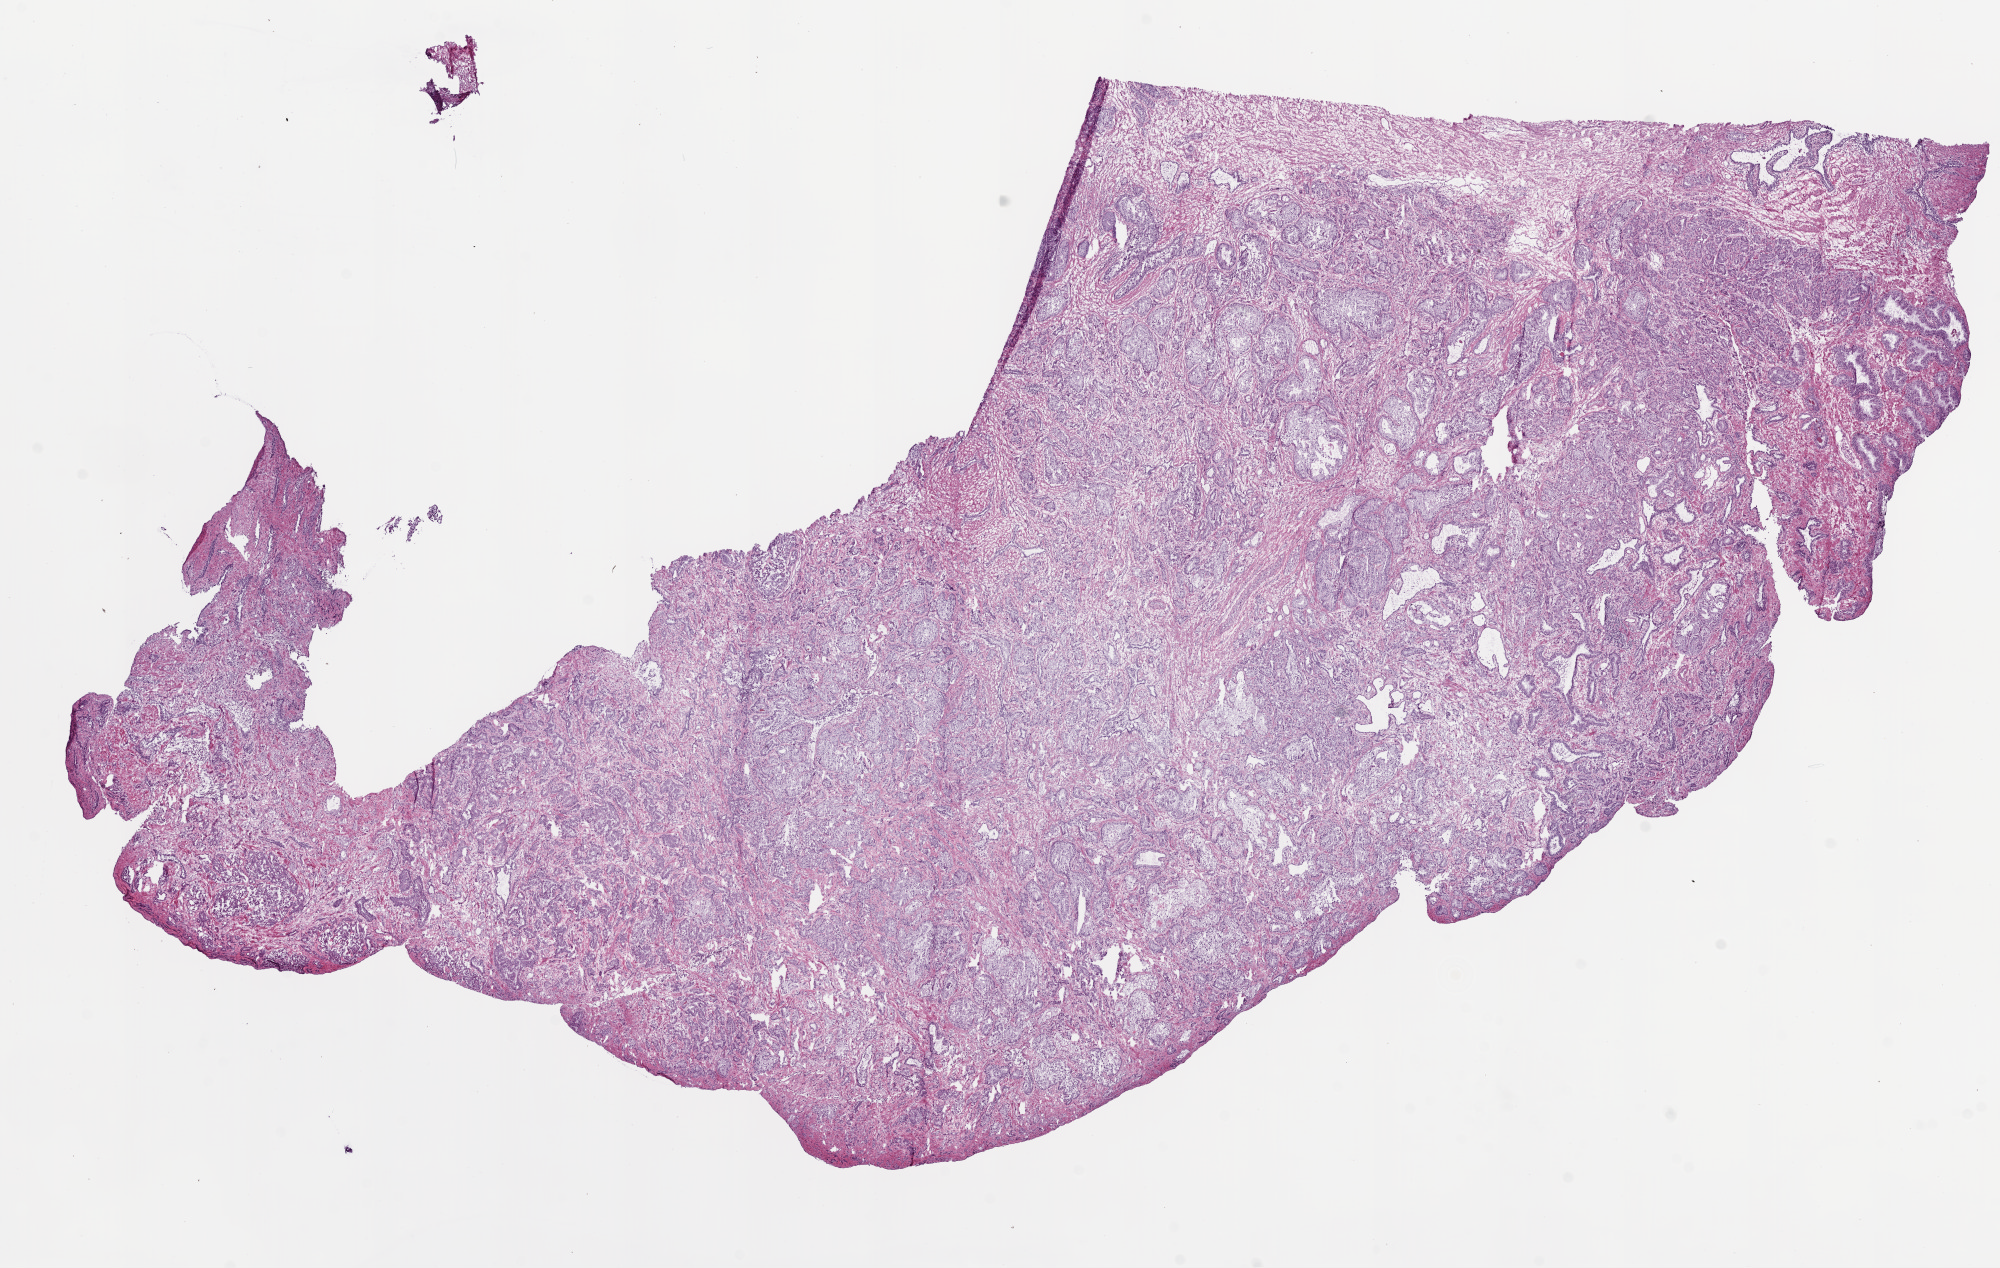
H&E whole-slide image — low-resolution overview of the scanned area, about 16.0 x 10.2 mm (slide scanned at 20x); frozen section from the bottom of the tissue portion; sample: primary tumour, prostate. Patient: male, age at initial diagnosis 49 years. Gleason score: 7 (3+4). Composition of this section per pathologist review: tumour cells 70%, tumour nuclei 75%, normal cells 10%, stromal cells 20%, necrosis 0%. Inflammatory infiltration, as recorded: lymphocyte infiltration 2%, monocyte infiltration 0%, neutrophil infiltration 0%.
Histologic diagnosis: Acinar cell carcinoma (prostate gland). Laterality: bilateral.